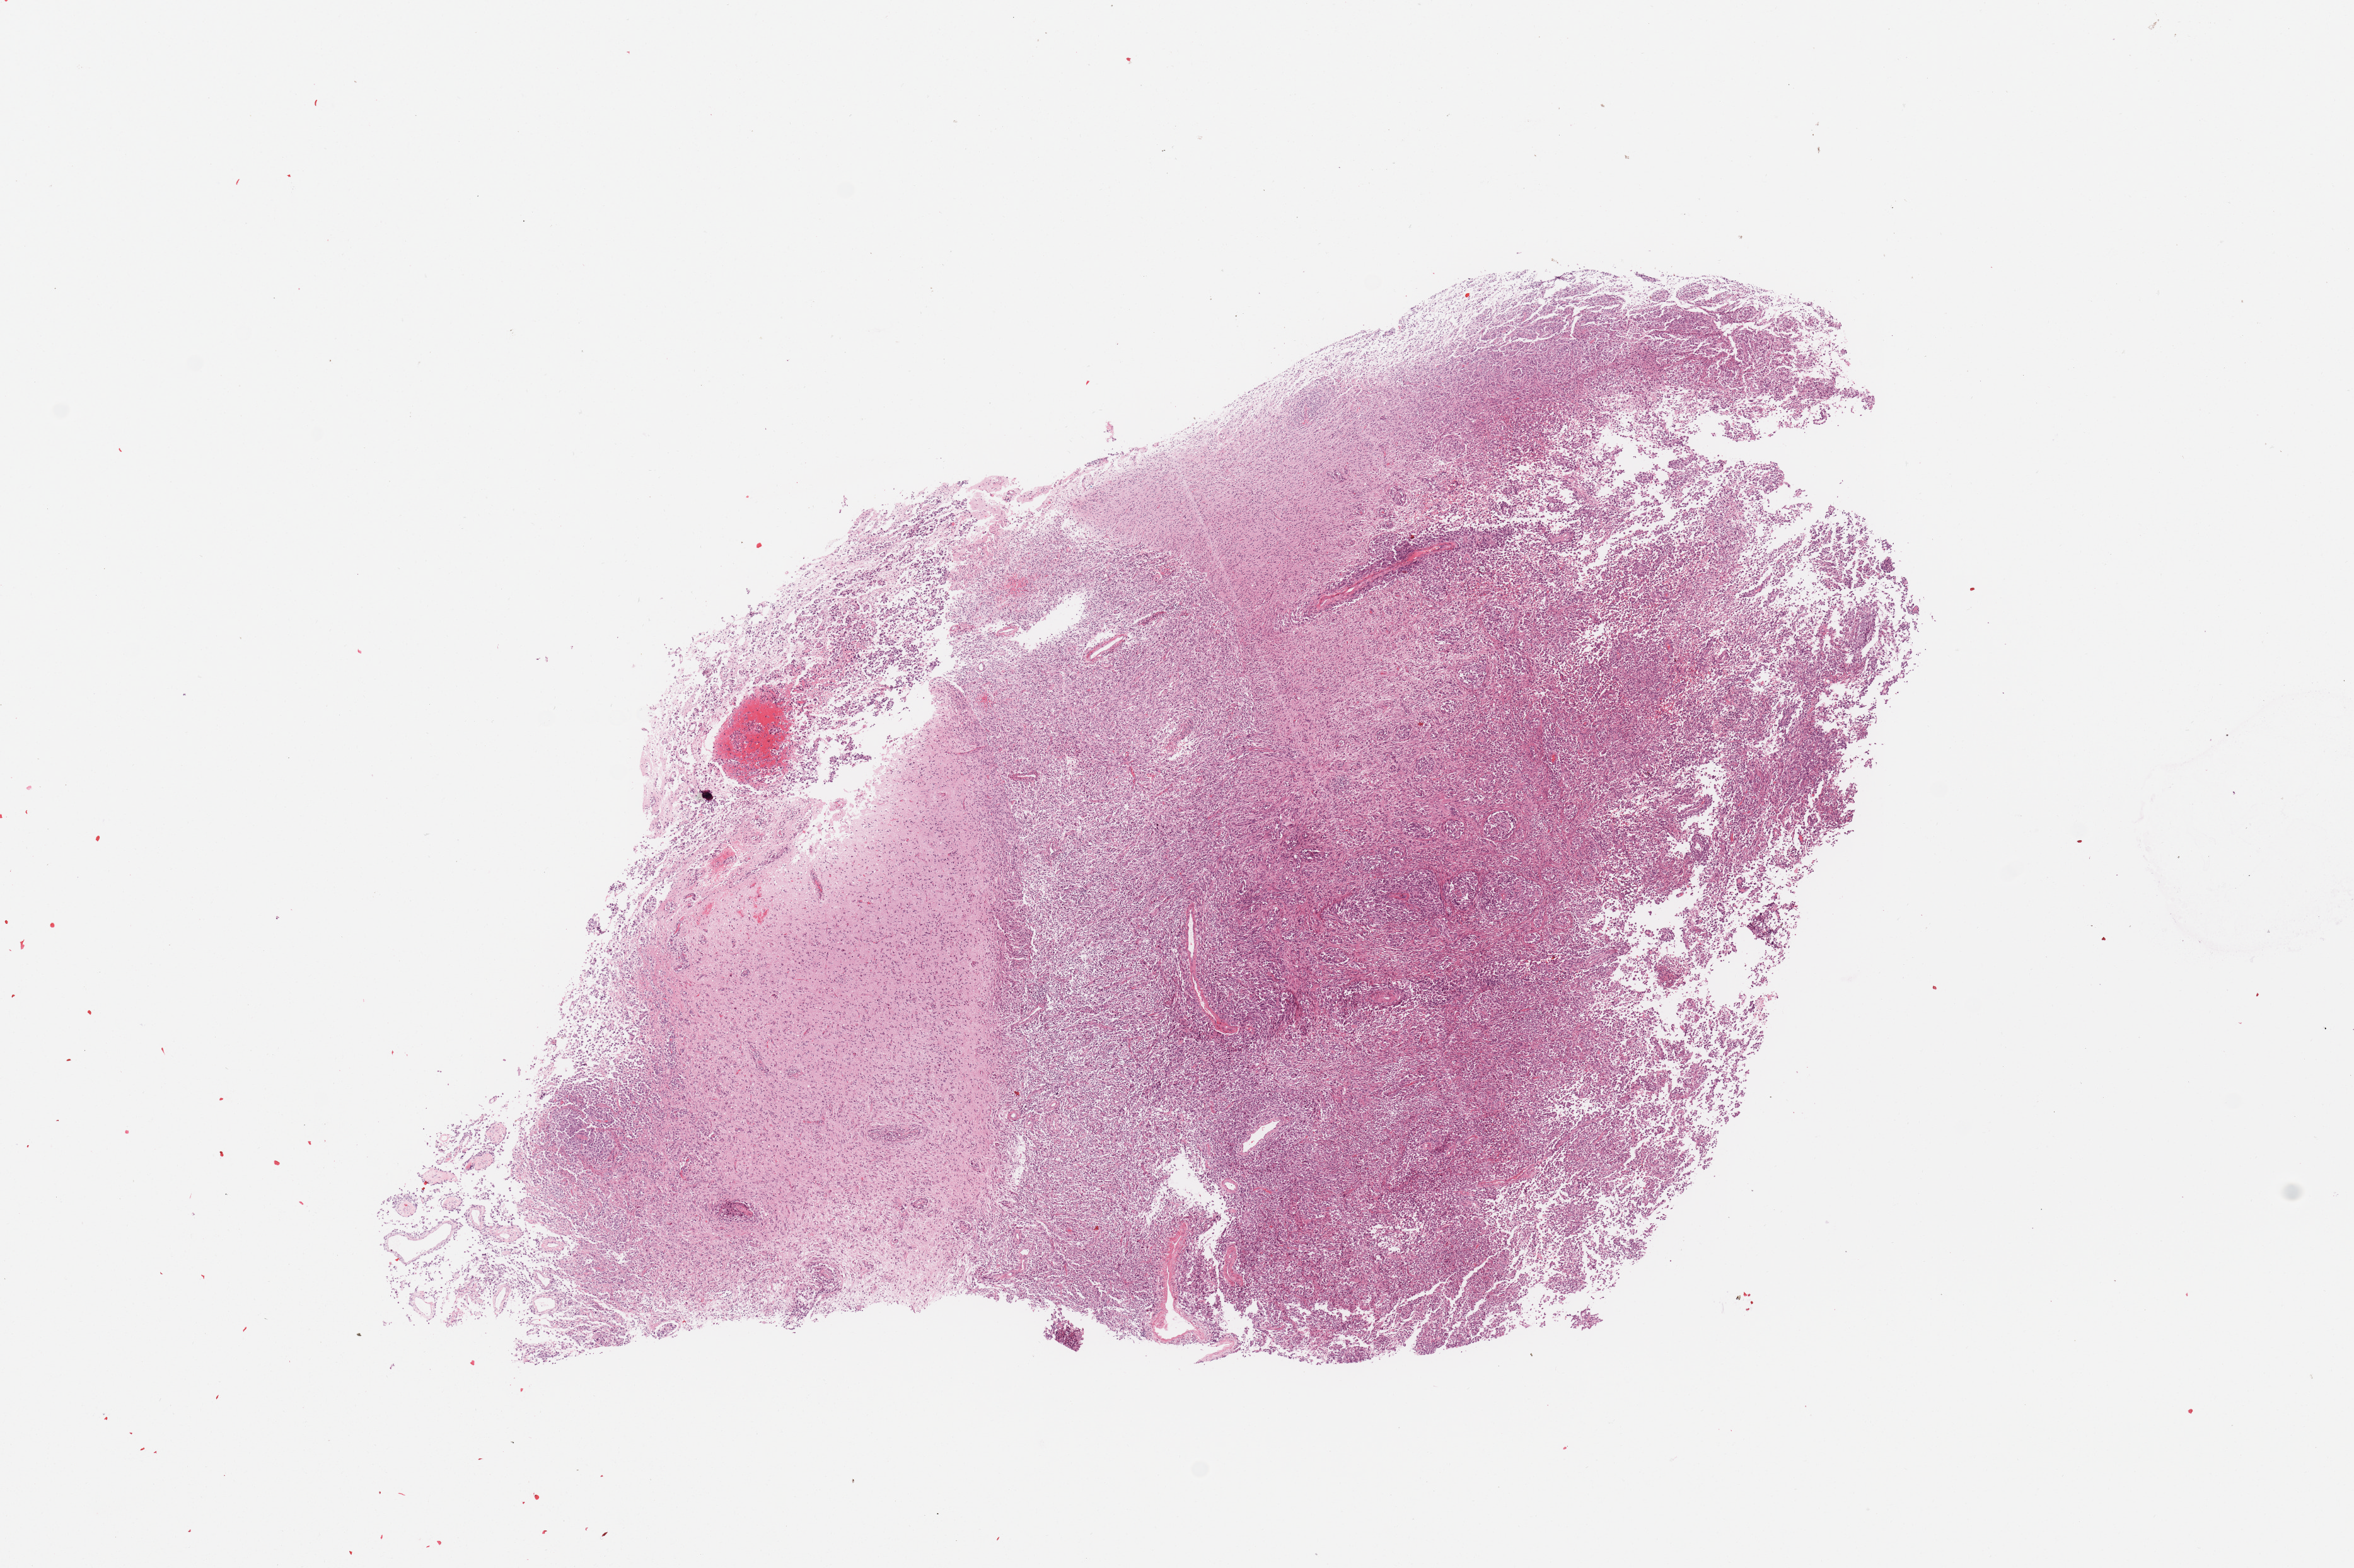
Whole-slide histology image, Hematoxylin and eosin (H&E) stained — a low-resolution overview of the entire scanned area, about 14.8 x 9.8 mm (slide scanned at 20x); tumour tissue sample, brain. 31-year-old female patient.
* diagnosis: Glioblastoma
* primary tumour site (as recorded): occipital lobe